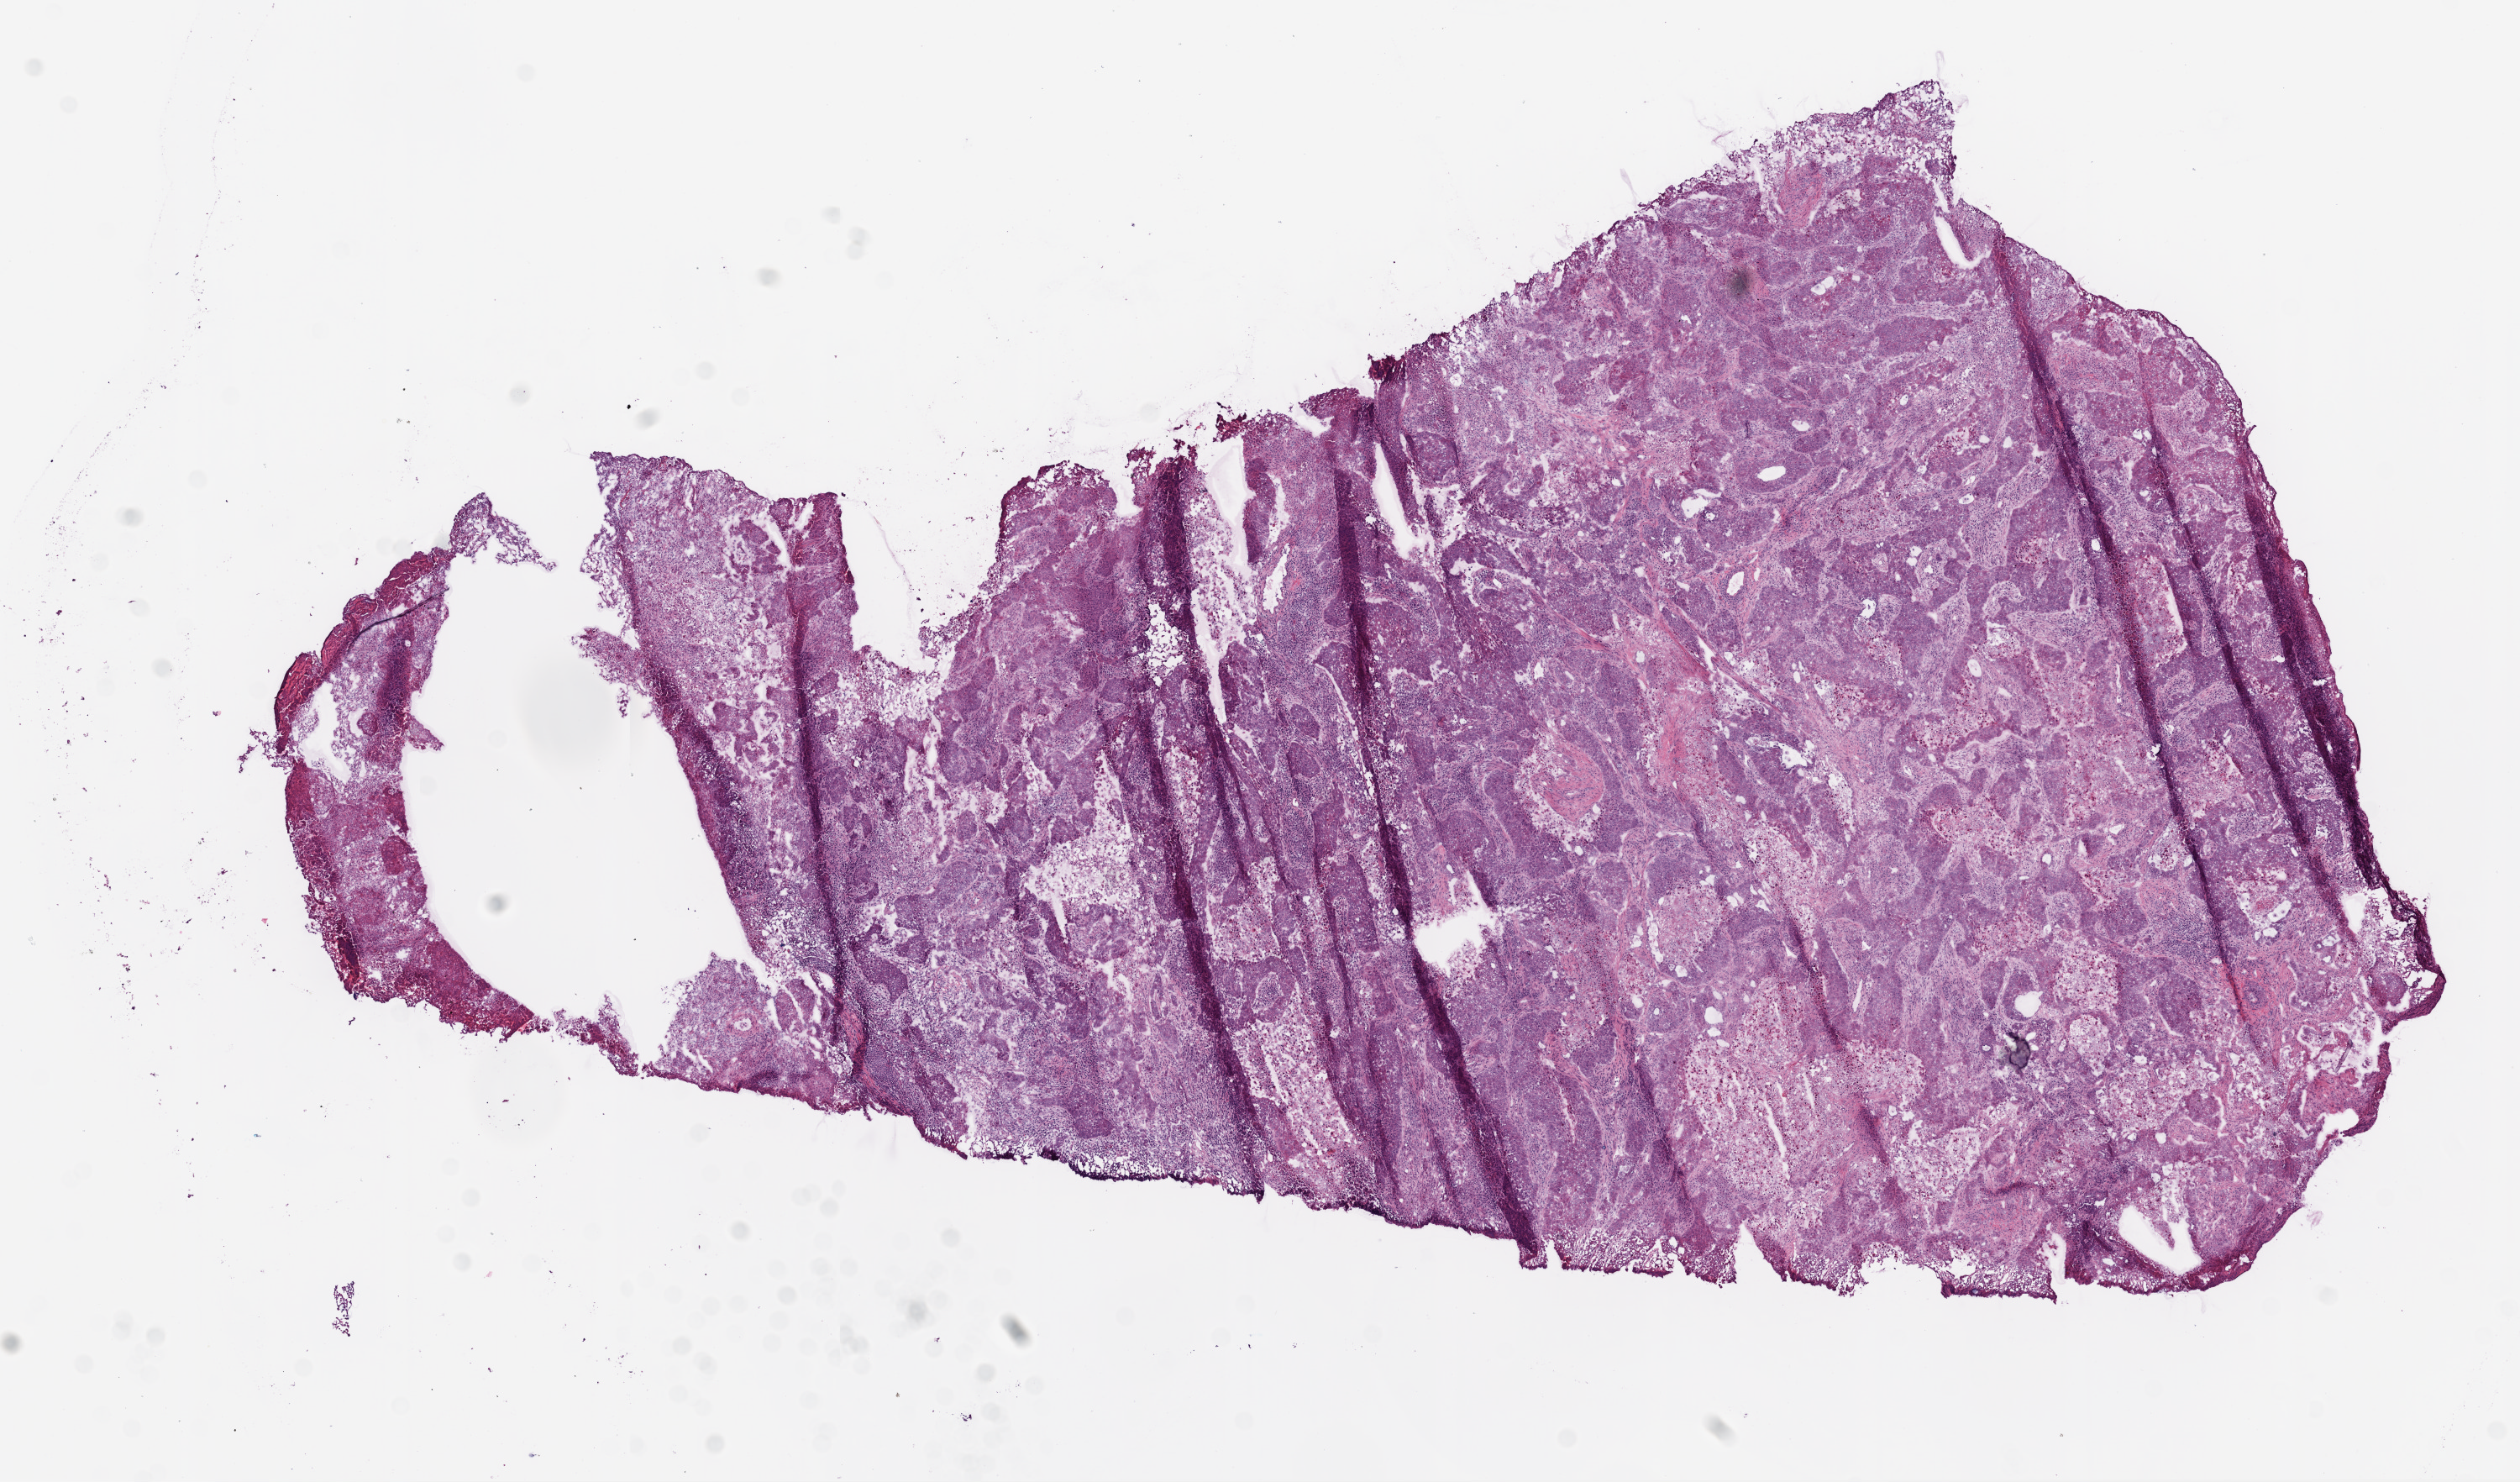
H&E whole-slide image, shown as a low-resolution overview of the whole scanned area (about 12.0 x 7.1 mm, acquisition: 20x scan); frozen section from the bottom of the tissue portion; sample: primary tumour, lung. Patient: female, age at initial diagnosis 74 years. Pathologist review of this section (percent, as recorded): tumour cells 72%, tumour nuclei 85%, normal cells 0%, stromal cells 10%, necrosis 18%.
AJCC pathologic stage: IB. Pathologic diagnosis: Squamous cell carcinoma, NOS. Laterality: right.